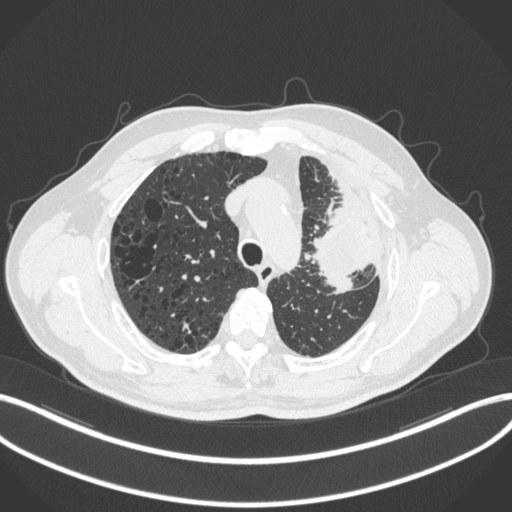
Chest CT, one axial slice; position 232 of 286 along the scan axis; reconstruction kernel B31f; 120 kVp; lung window (W 1500 / L -600 HU); 1 mm slice thickness; 512 × 512 image matrix, field of view 400 × 400 mm. Male patient, age 68 years. Case-level facts recorded for this patient, not image findings: clinical TNM (as recorded): T3 N3 M1.
Outlined on this slice (bounding box drawn by a radiologist):
- lung tumour (recorded histology: adenocarcinoma): bounding box [x1, y1, x2, y2] px = [313, 184, 368, 299]